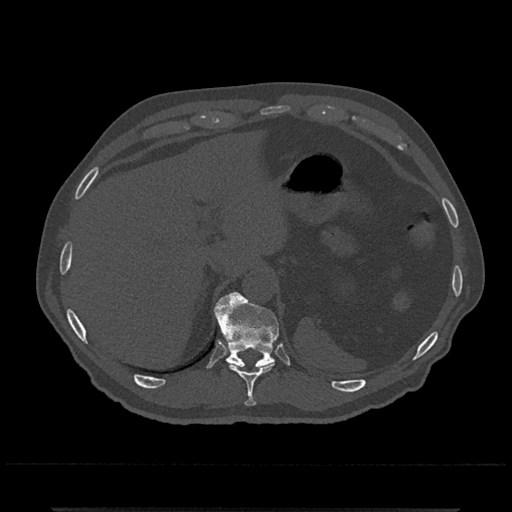
CT including the spine, one axial slice; slice 524 of 797 in the series (ordered by position); bone window (W 1800 / L 400 HU); 0.5 mm slice thickness; 512 × 512 image matrix, field of view 393 × 393 mm. Male patient, age 67 years. Case-level facts recorded for this patient, not image findings: primary cancer: prostate.
Annotated regions visible in this slice (semi-automatic segmentation, software-assisted and operator-edited):
- T10 vertebra: bounding box <231,364,274,407> (left, top, right, bottom; pixels)
- T11 vertebra: <214,293,279,368>